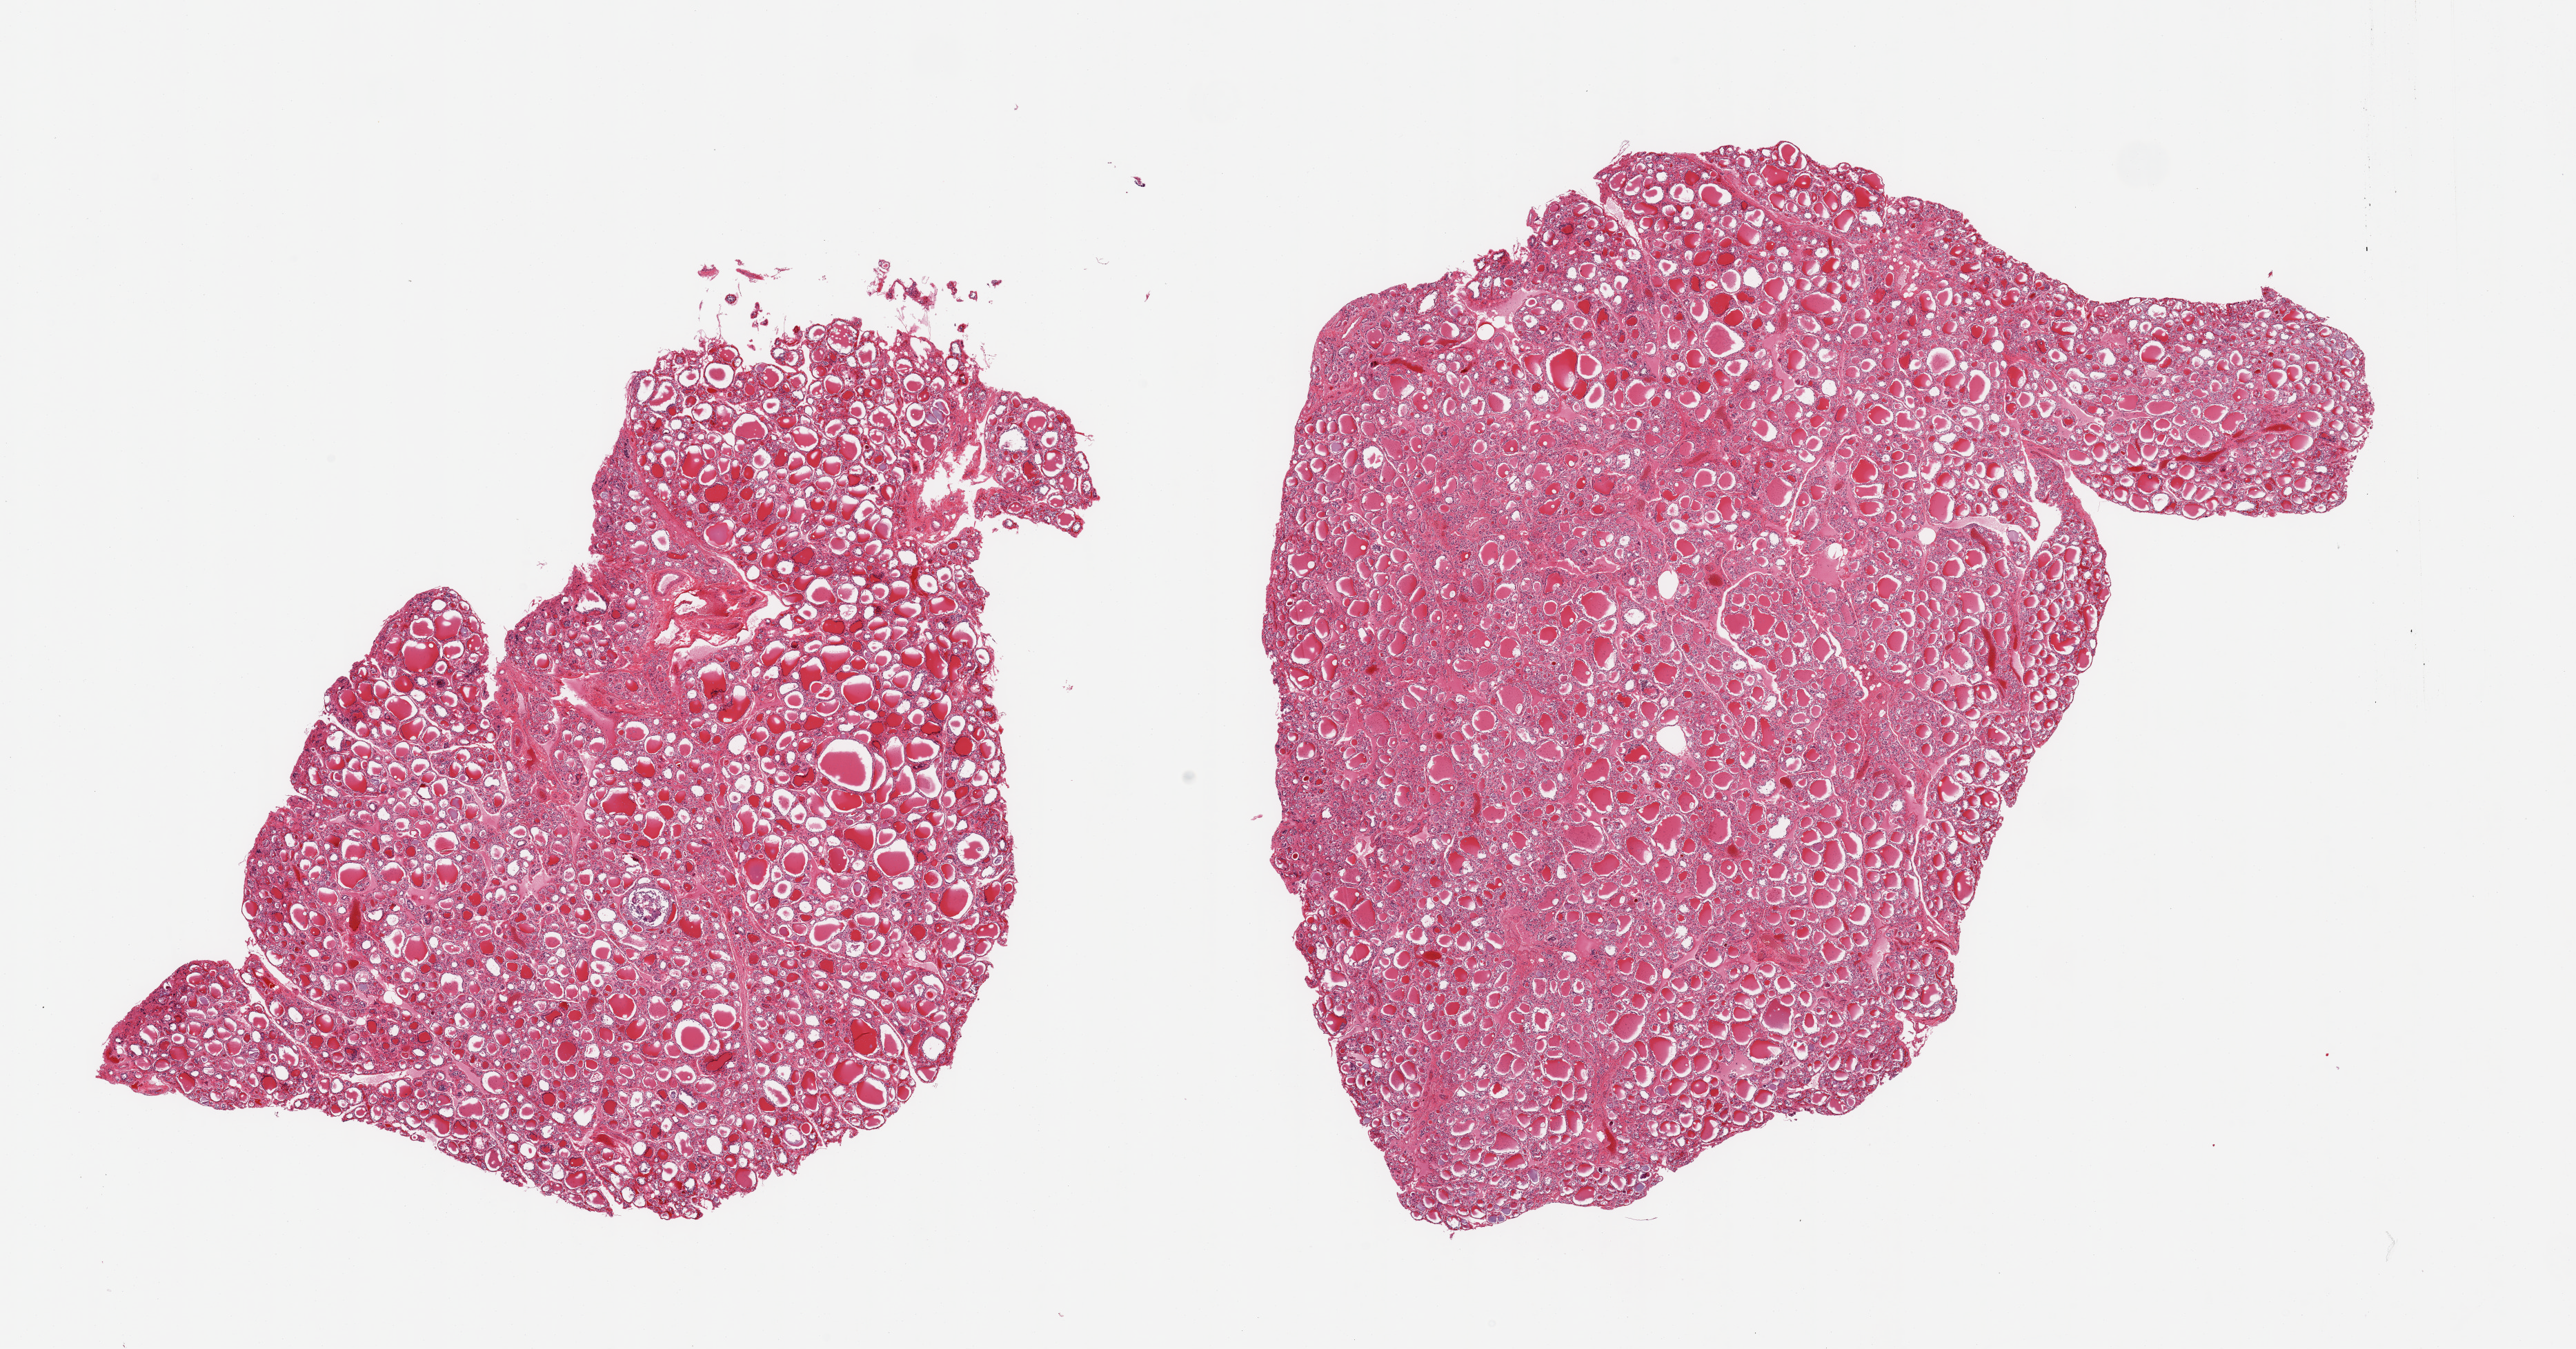
Whole-slide image, hematoxylin and eosin (H&E) stain, a low-resolution overview of the entire scanned area, about 29.5 x 15.5 mm; PAXgene-fixed paraffin-embedded (PFPE) section; target tissue: thyroid; donor tissue sample. Donor sex: male.
• pathologist's review note for this sample: 2 pieces, no abnormalities